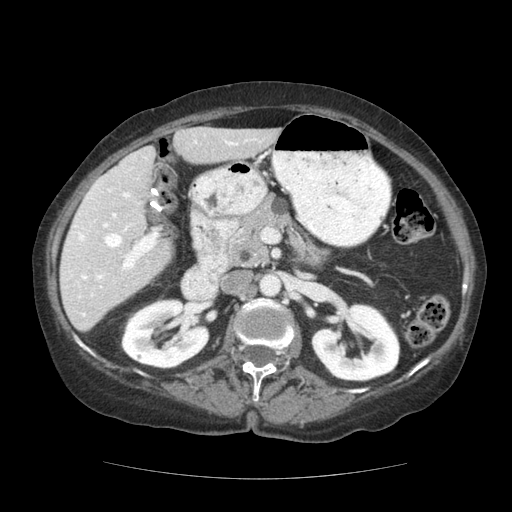
Contrast-enhanced abdominal CT (liver protocol), one axial slice; slice 63 of 111 in the series (ordered by position); reconstruction kernel STANDARD; soft-tissue window (W 400 / L 40 HU); 2.5 mm slice thickness; 512 × 512 image matrix, field of view 360 × 360 mm. Case-level facts recorded for this patient, not image findings: diagnosis: hepatocellular carcinoma (patient treated with transarterial chemoembolisation; whether this scan precedes or follows treatment is not stated here); TNM stage (as recorded): Stage-I; Child-Pugh class: A; tumour differentiation: moderately-poorly differentiated; tumour size: 7.3 cm.
Outlined on this slice (semi-automatically segmented with operator editing):
- liver parenchyma outside the tumour (the mass and vessels are separate outlines, so this box may not span the whole liver): bounding box [x1, y1, x2, y2] px = [60, 126, 280, 330]
- liver vessels: [68, 139, 256, 316]